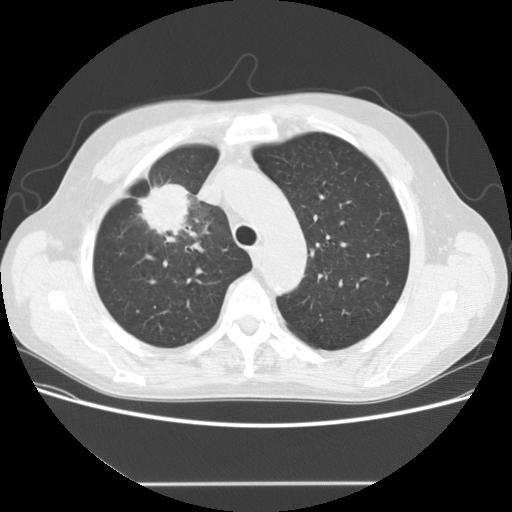
Chest CT (low-dose screening protocol), one axial image. Baseline screening round. Lung window (W 1500 / L -600 HU). 2.5 mm slice thickness. 120 kVp. Slice 37 of 153 in the series. 512 × 512 image matrix. Male participant, aged 56 years at enrolment. Current smoker at enrolment.
Expert-annotated lung lesion, bounding box [x1, y1, x2, y2] px = [128, 173, 213, 245]. The screening reader recorded 2 non-calcified nodules or masses ≥4 mm on this exam (right upper lobe, right middle lobe); which of them this box marks is not recorded. Lung cancer was diagnosed 120 days after this screen: adenocarcinoma, NOS, right upper lobe, stage IIIA (AJCC 6th edition), 34 mm at pathology.